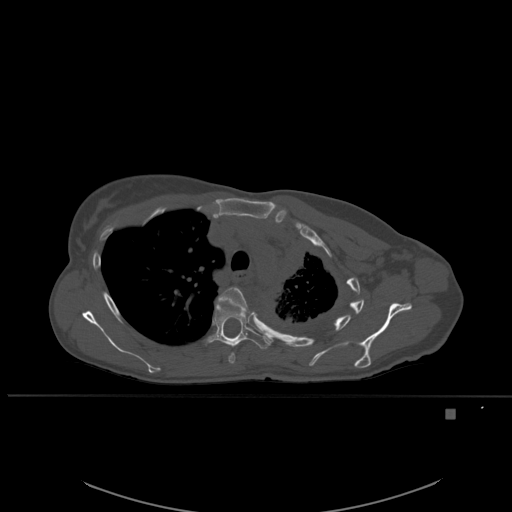
CT including the spine, one axial slice; position 403 of 537 along the scan axis; bone window (W 1800 / L 400 HU); 1.5 mm slice thickness; 512 × 512 image matrix. Patient: female, 45 years. Case-level facts recorded for this patient, not image findings: primary cancer: lung.
Annotated regions visible in this slice (semi-automatically segmented with operator editing):
- T4 vertebra: bounding box [x1, y1, x2, y2] px = [218, 287, 248, 364]
- T5 vertebra: [207, 300, 270, 349]